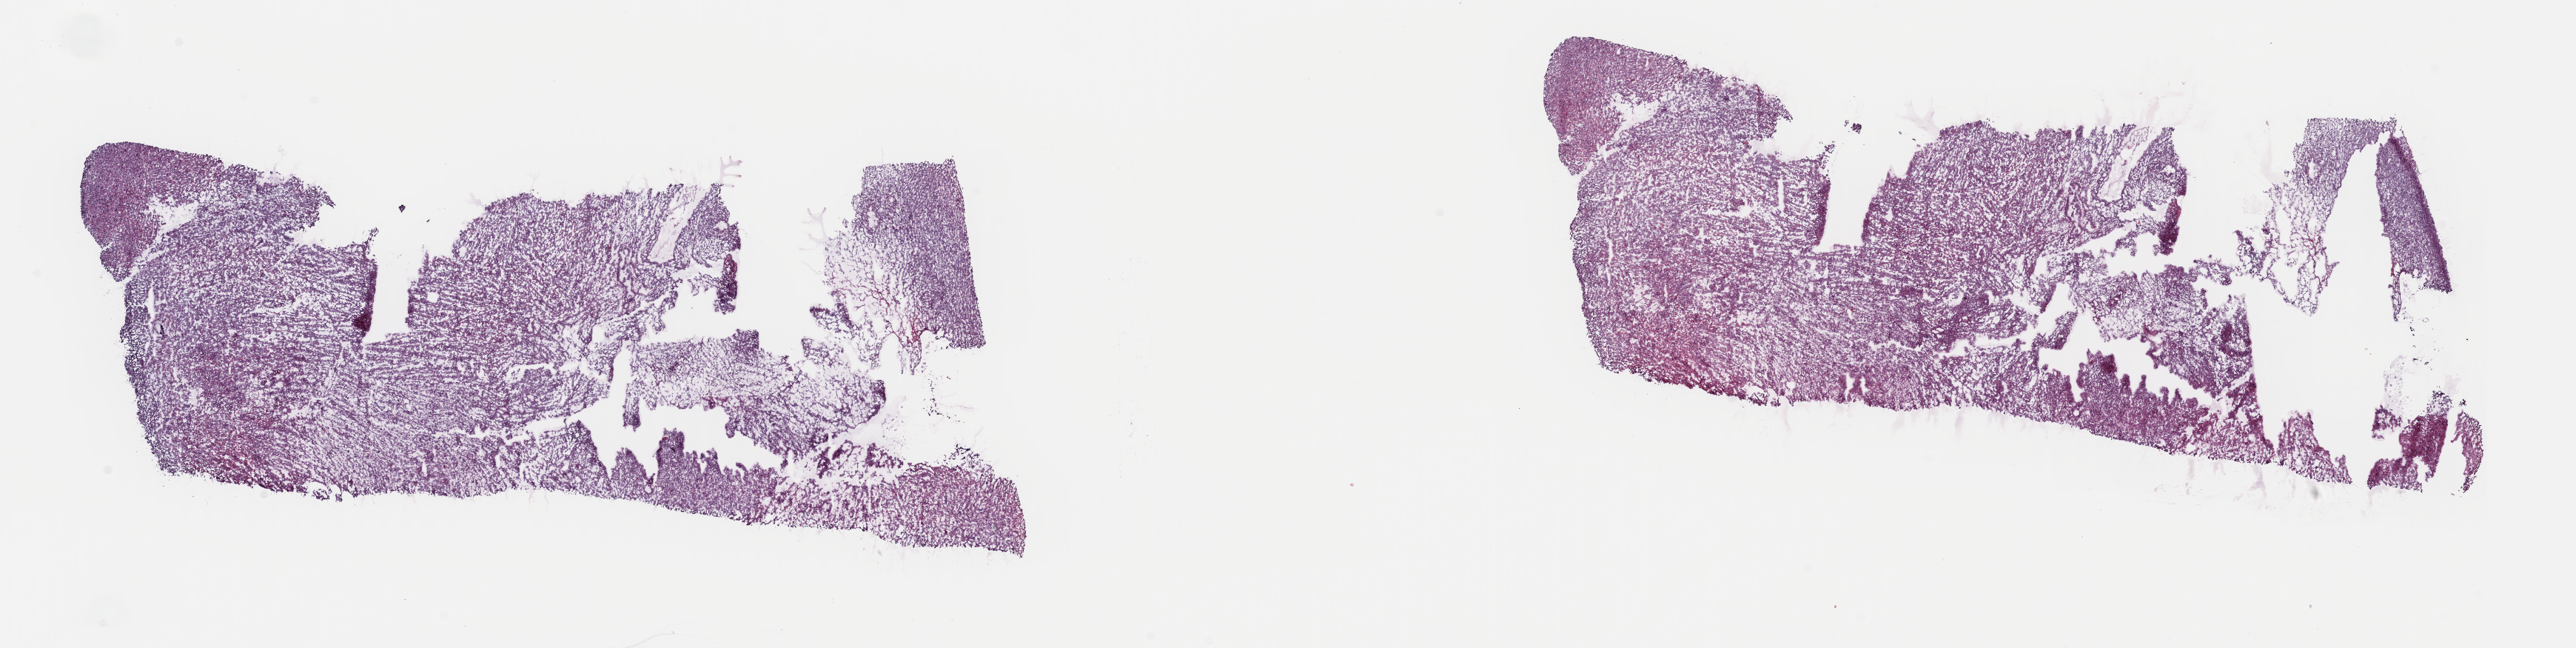
Digitized H&E-stained tissue section (whole slide), whole scanned area (about 27.5 x 6.9 mm, from a 40x scan) shown as a low-resolution overview. Frozen section from the top of the tissue portion. Uterus, primary tumour sample. Female, age 77 years at initial diagnosis. Slide review estimates, as recorded: tumour cells 100%, tumour nuclei 80%, normal cells 0%, stromal cells 0%, necrosis 0%. Infiltration values recorded for this section: lymphocyte infiltration 2%, monocyte infiltration 0%, neutrophil infiltration 0%.
Histologic diagnosis: Mullerian mixed tumor (fundus uteri). FIGO stage: IIIA.